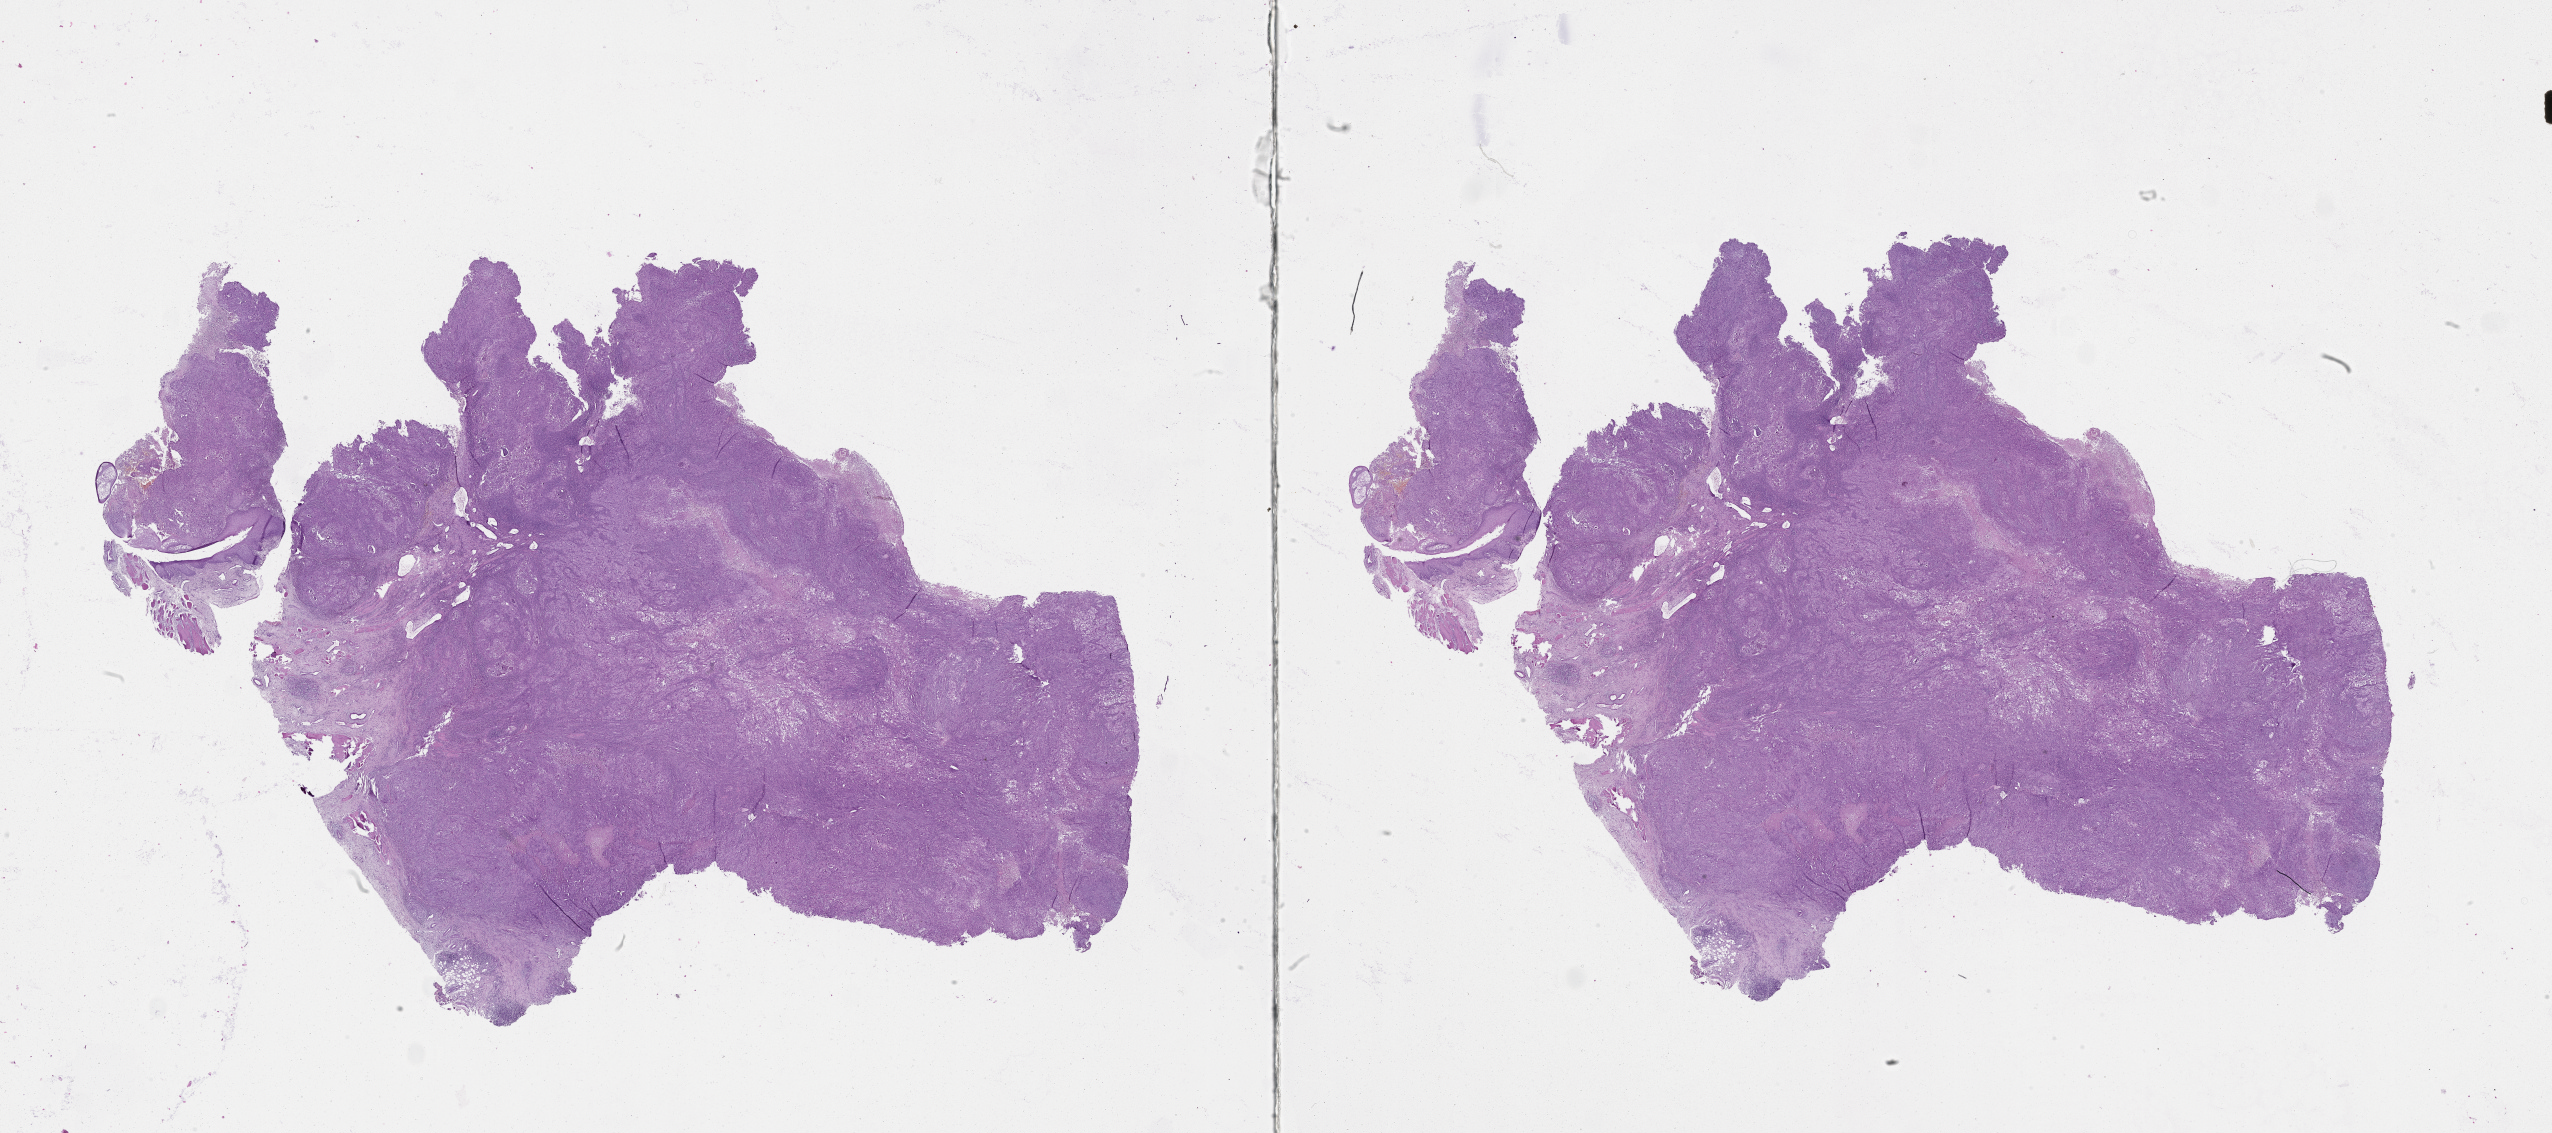
Digitized H&E-stained tissue section (whole slide), a low-resolution overview of the entire scanned area, about 41.1 x 18.2 mm, head and neck, tissue type not recorded. Male, 55 y/o.
Patient diagnosis: Squamous cell carcinoma, NOS (larynx, NOS).